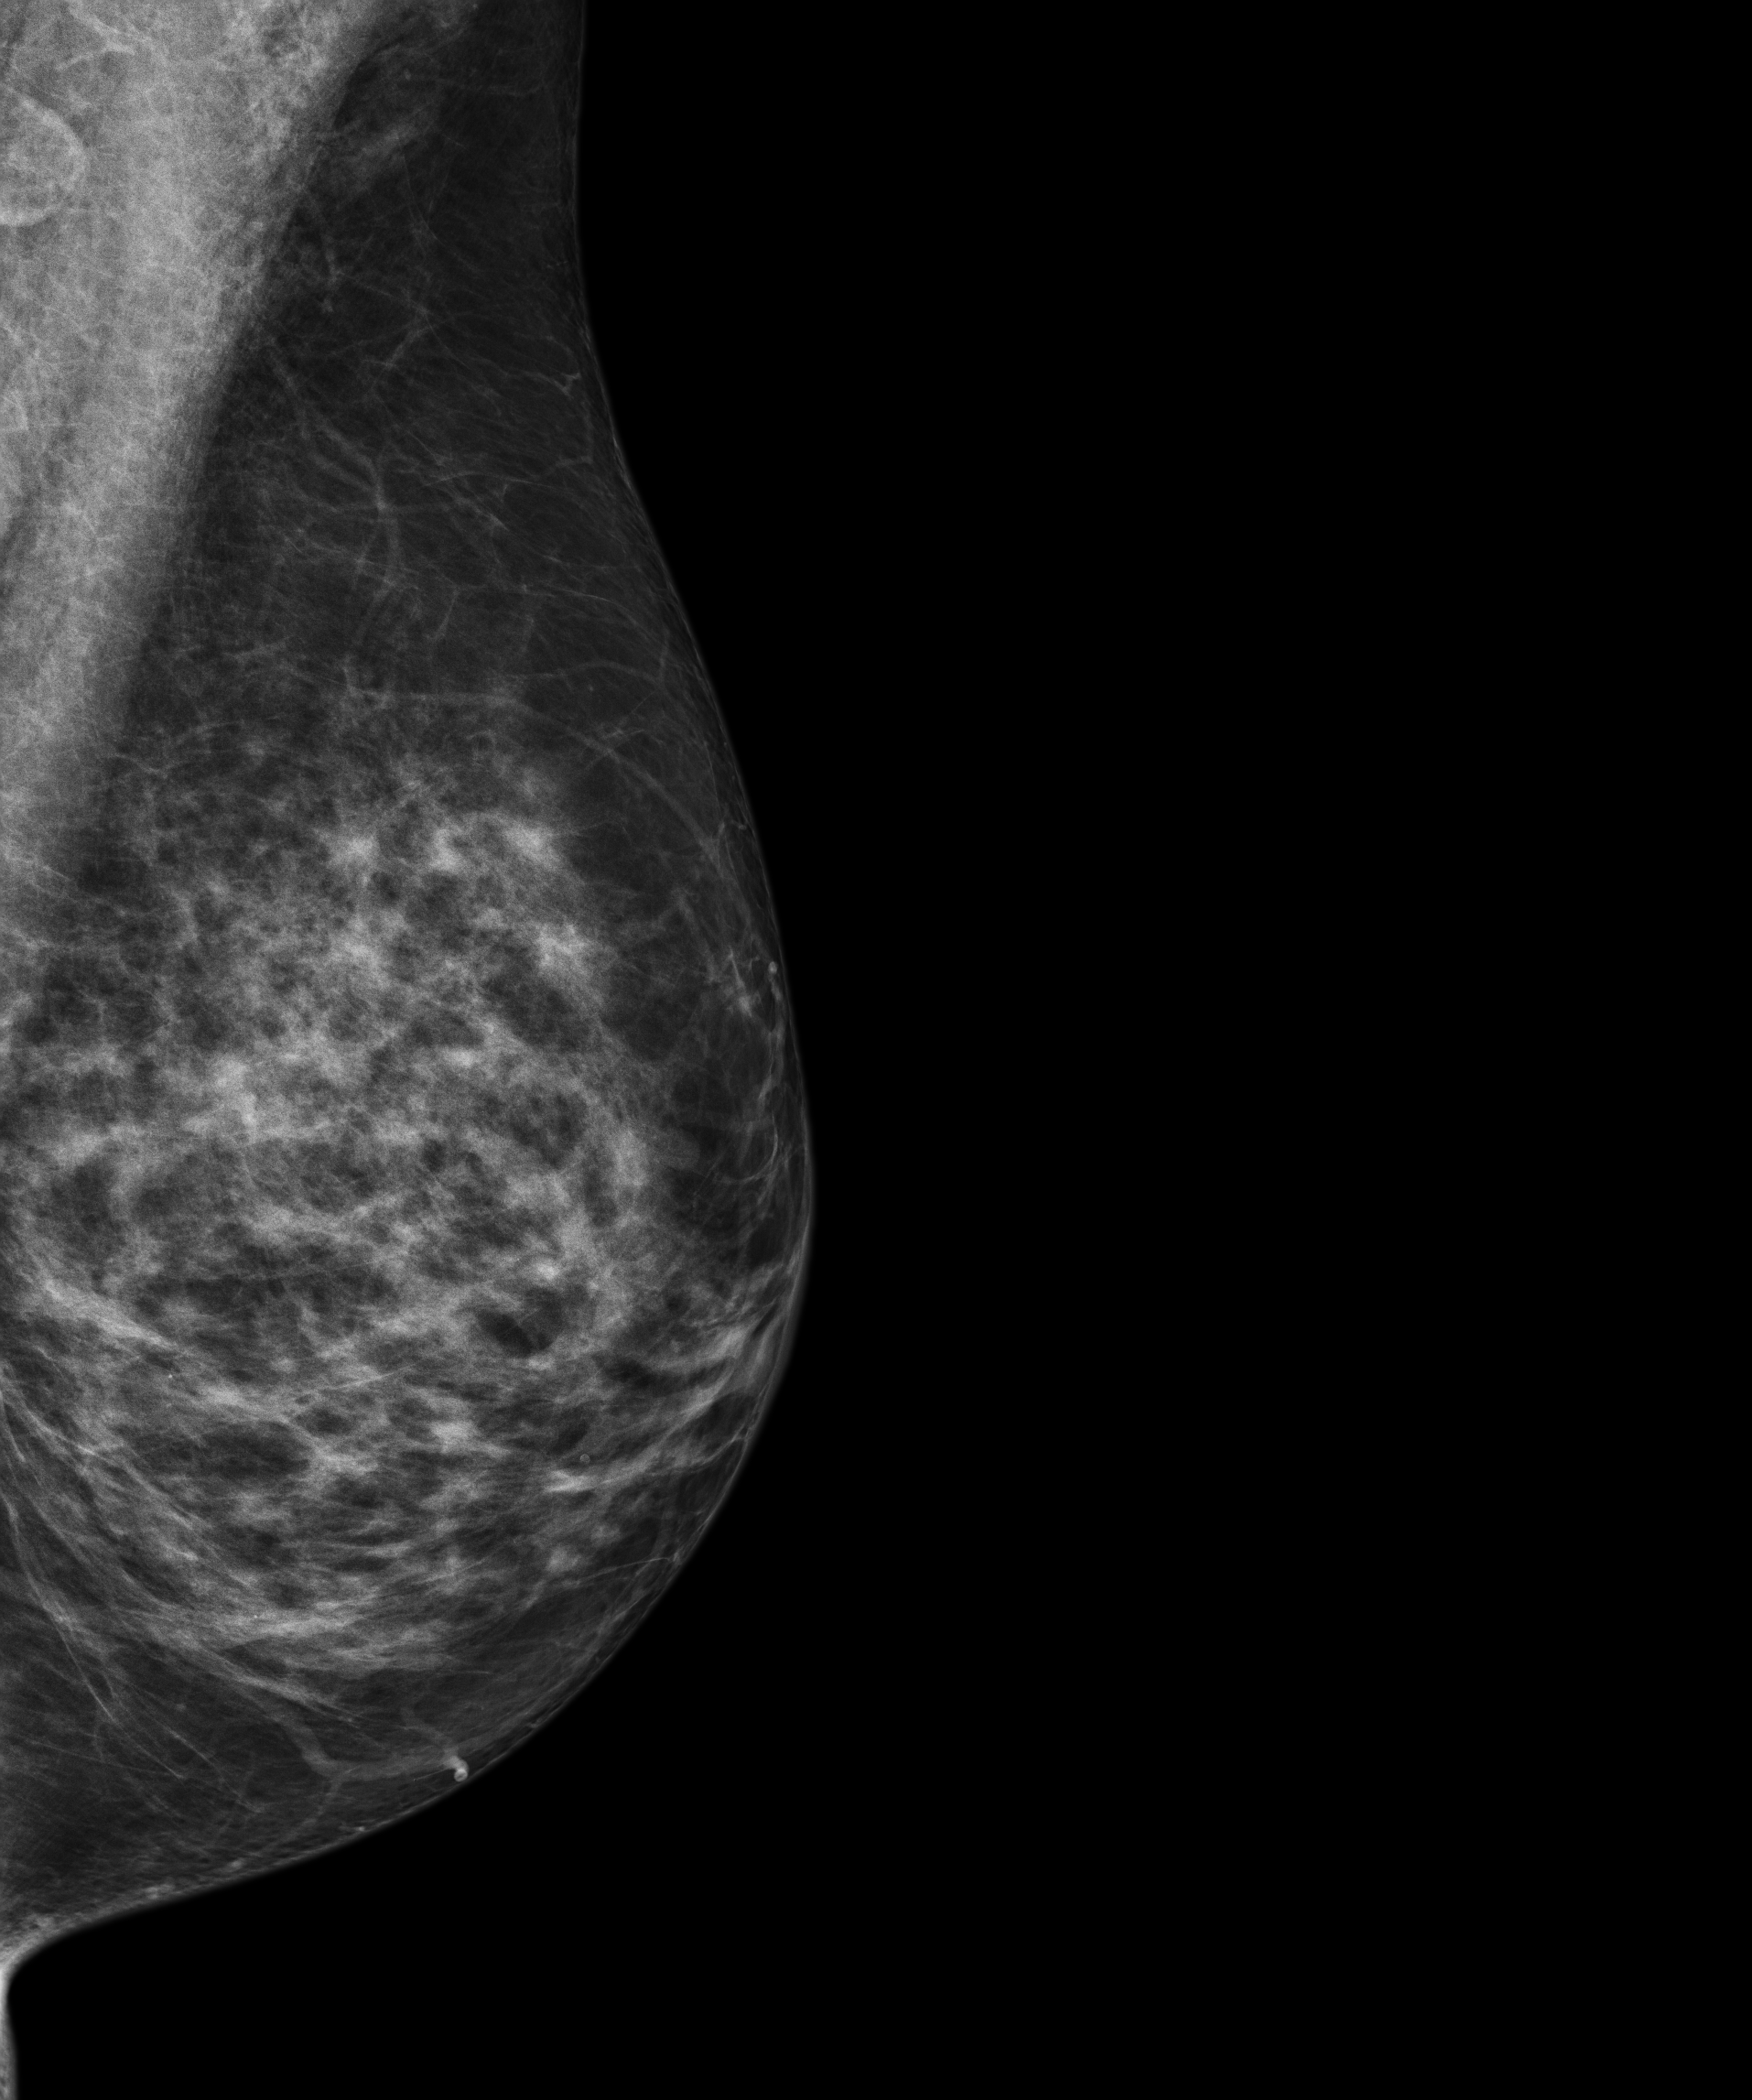
Full-field digital mammogram (FFDM); left breast; mediolateral oblique (MLO) view; screening examination; compressed breast thickness 60 mm. Patient aged 58 years (female).
Final BI-RADS category for the screening round (tomosynthesis exam, both breasts): category 1.